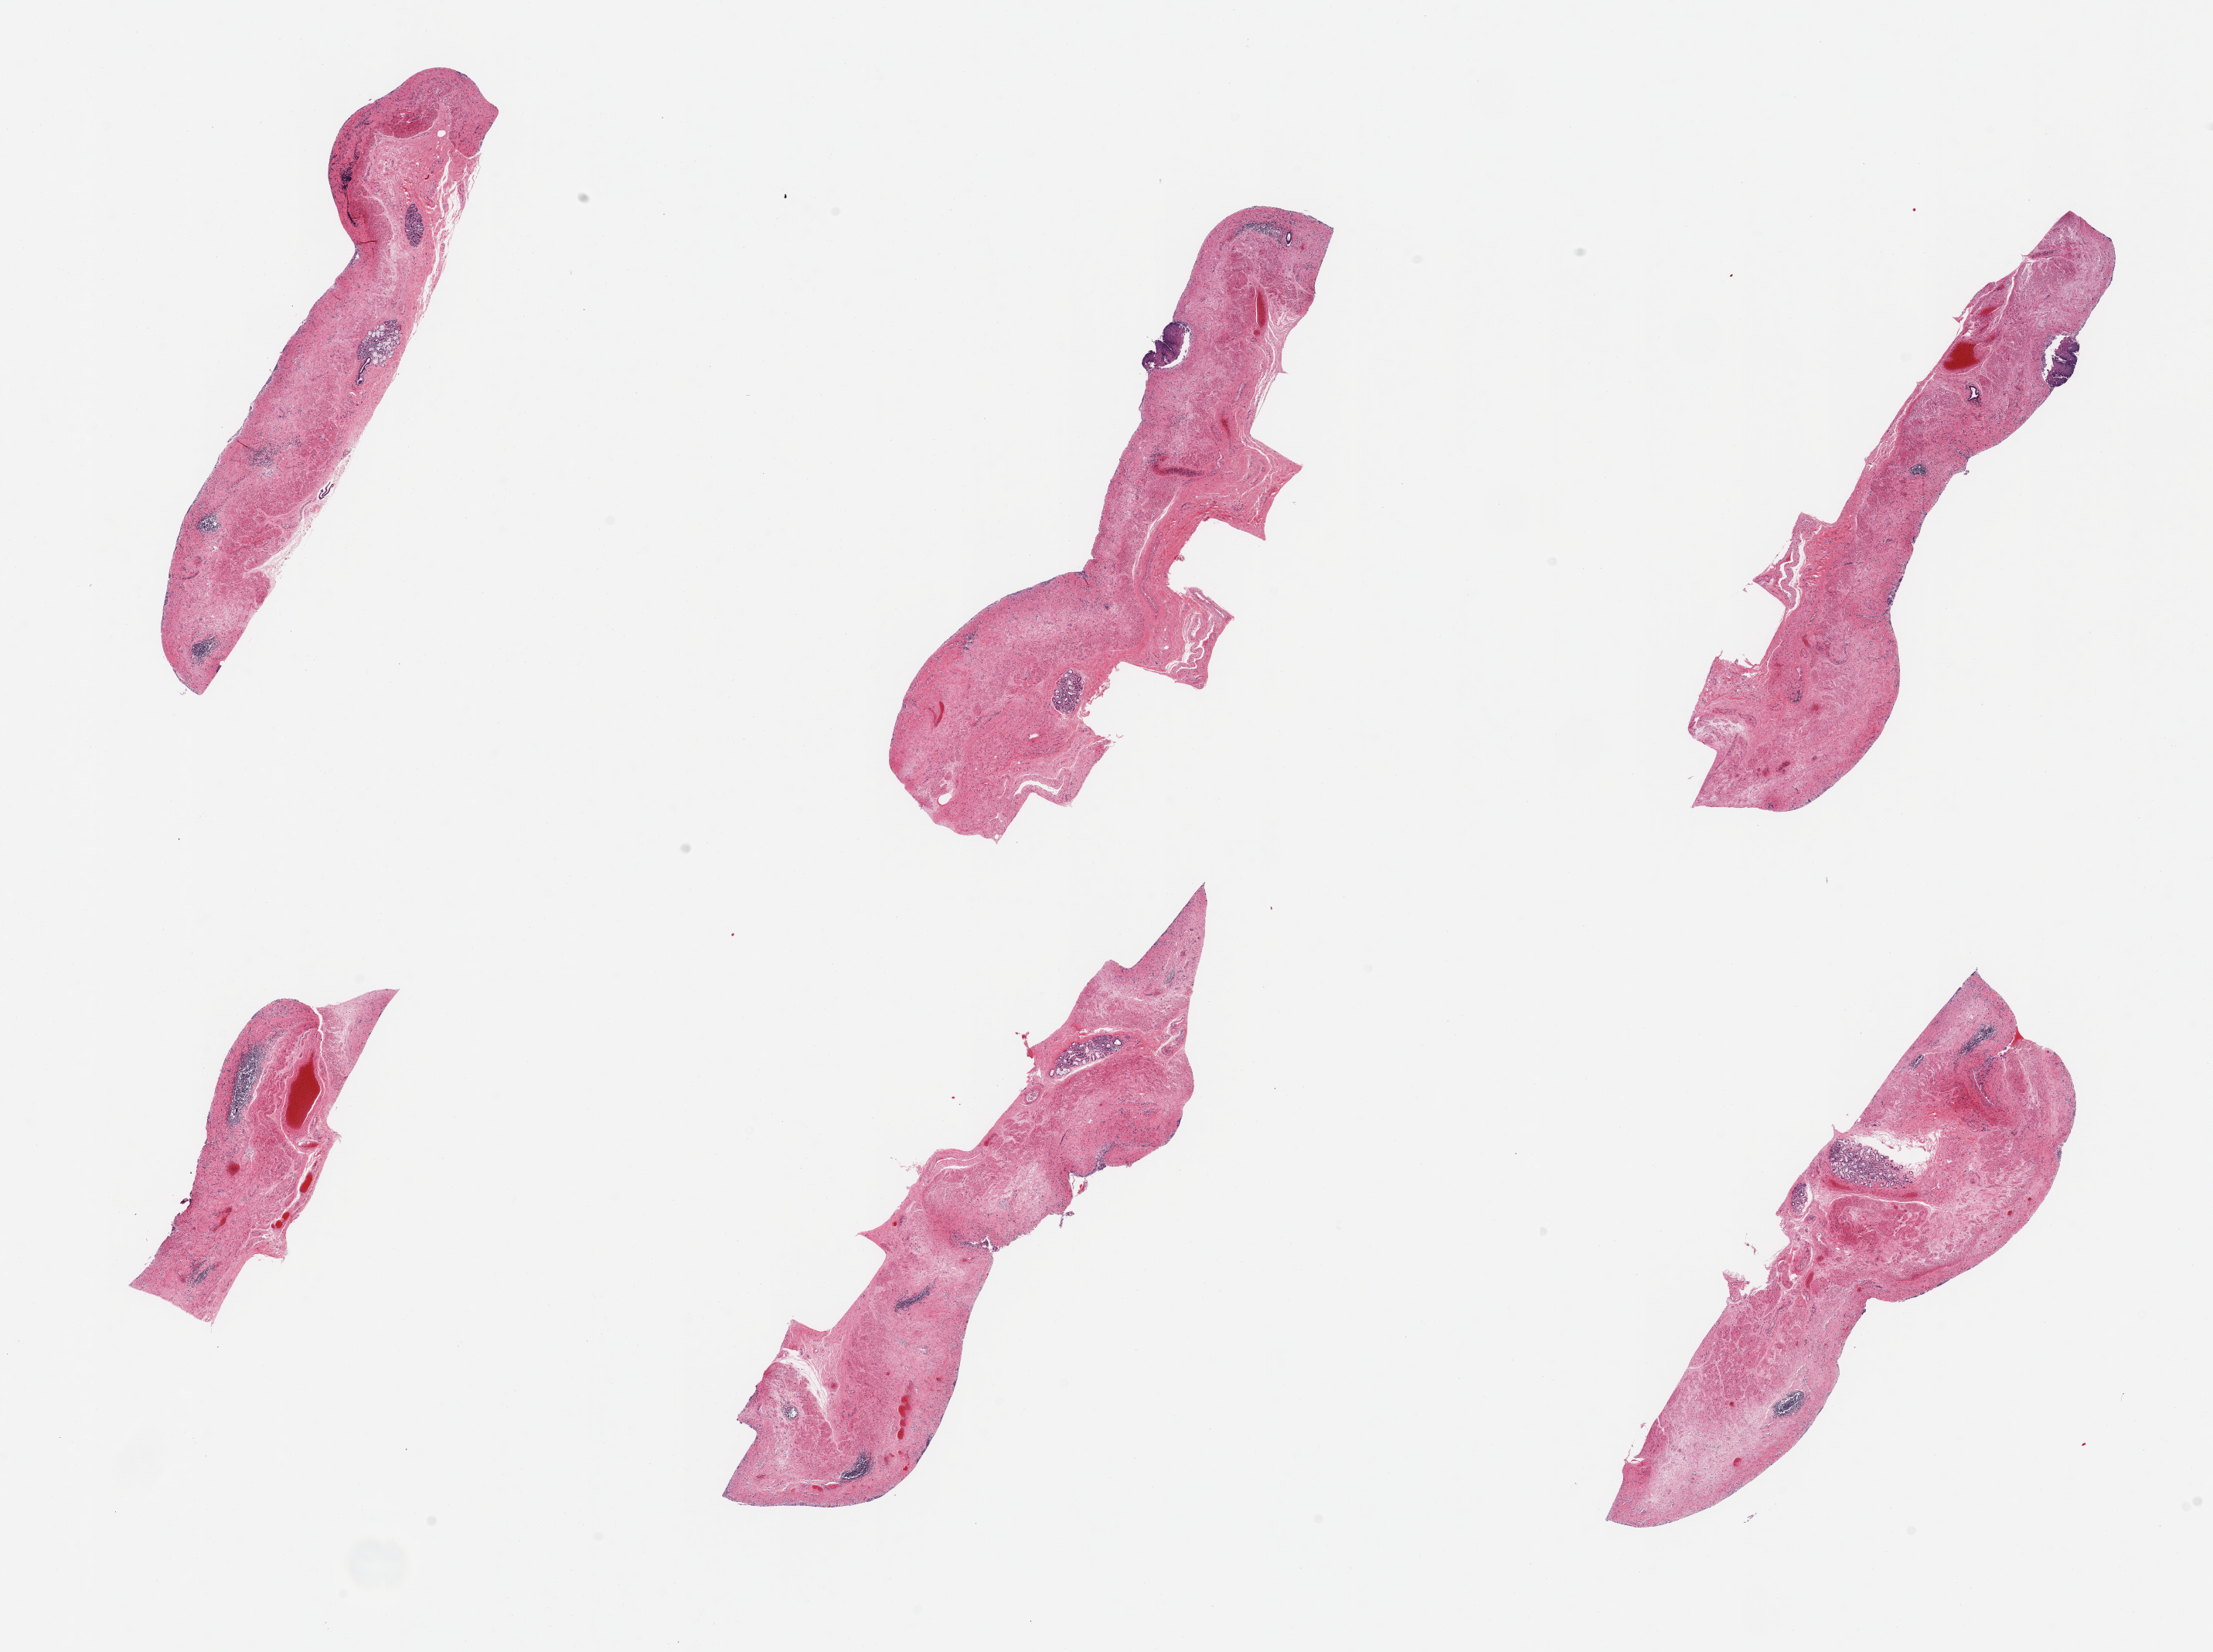
Digitized hematoxylin and eosin (H&E)-stained section, brightfield, shown as a low-resolution overview of the whole scanned area (about 22.6 x 16.9 mm, acquisition: 20x scan); PAXgene-fixed, paraffin-embedded tissue; section of esophageal mucous membrane (target tissue); tissue donor sample. Donor sex: male.
Reviewer comment on this tissue sample: 6 pieces; mucosa absent/autolyzed and moderately autolyzed submucosa, submucosal glands, minute fragments of residual squamous epithelium; scattered lymphoid aggregates in submucosa.